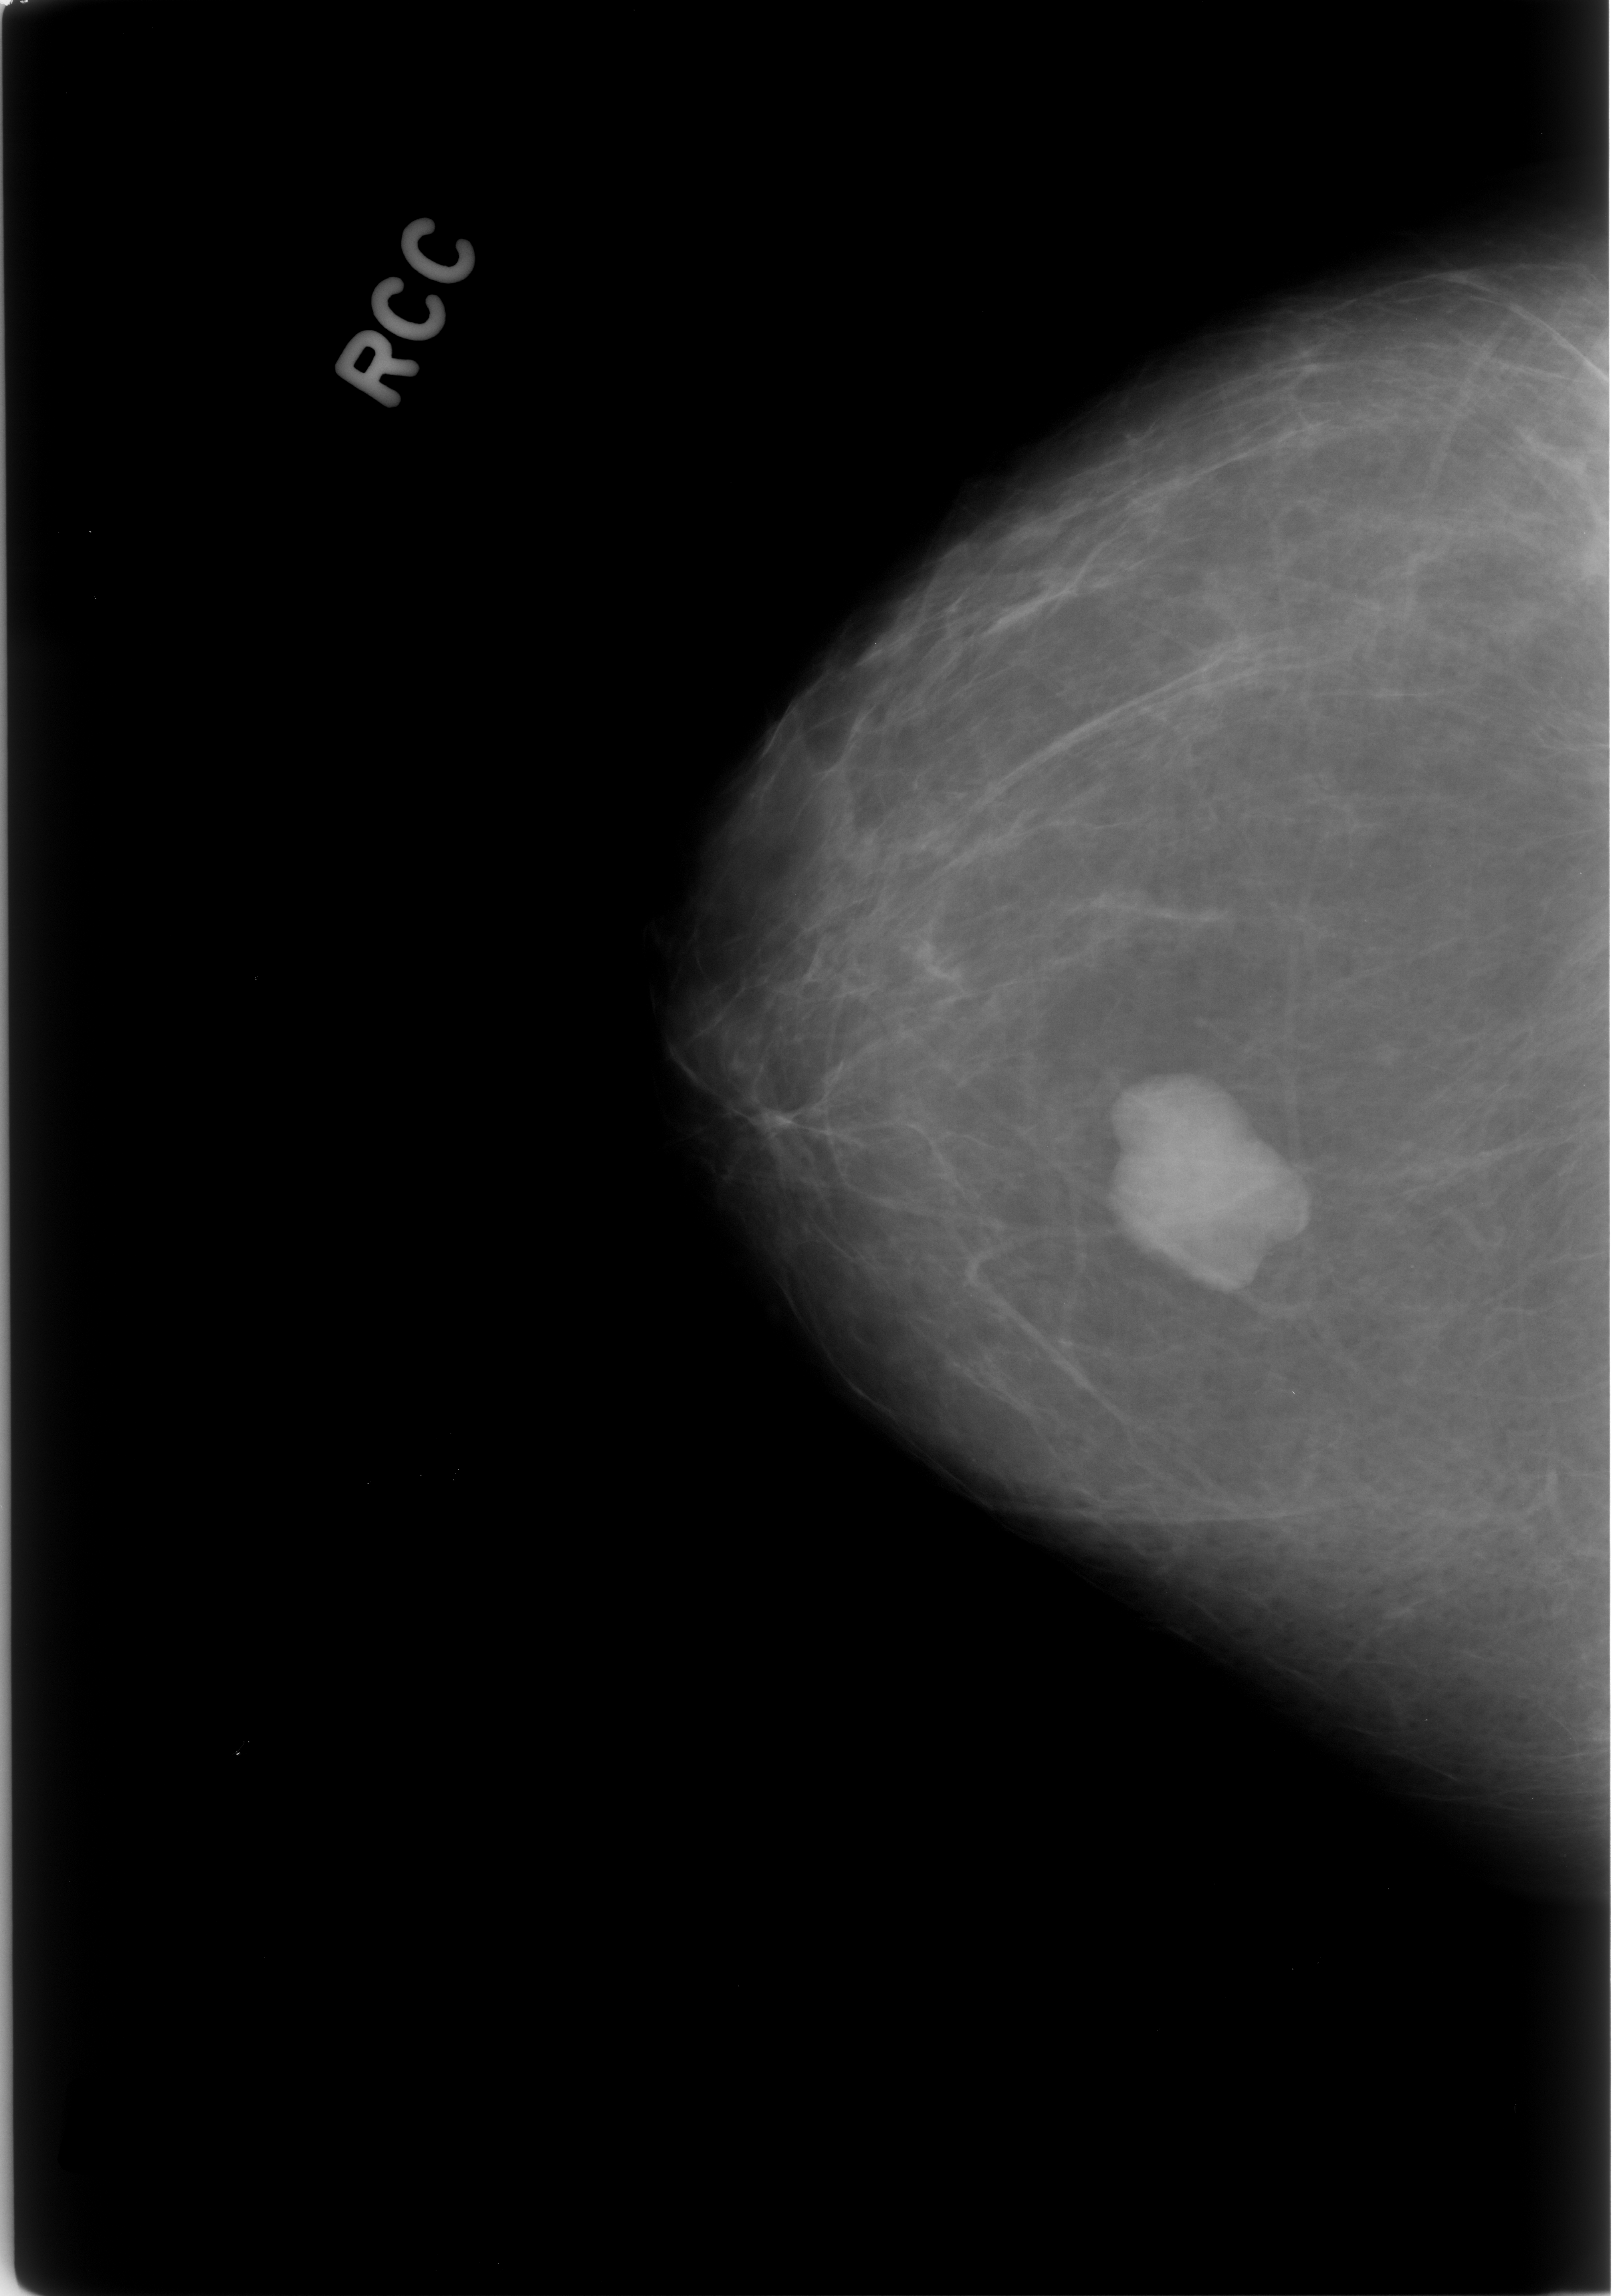
Digitized screen-film mammogram. Right breast. CC view. BI-RADS breast density category 1 (scale 1–4). 1613 × 2296 image matrix.
Expert-marked regions of interest on this film, with their recorded descriptors:
- mass, shape lobulated, margins circumscribed; BI-RADS assessment category 4; subtlety rating 5 on a 1 (subtle) to 5 (obvious) scale; pathology (as recorded): benign: box from (x=1102, y=1073) to (x=1303, y=1275) px